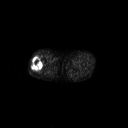
FDG PET of an extremity soft-tissue mass (from a PET/CT study), one axial slice. Slice 241 of 267 in the series (ordered by position). 3.27 mm slice thickness. 128 × 128 image matrix, field of view 700 × 700 mm. Male patient, age 43 years. From the clinical record (not read from this slice): histological type: poorly differentiated synovial sarcoma; grade: high; site of the primary tumour: right buttock.
Outlined on this slice (expert contour drawn on MRI and transferred to this co-registered scan by the dataset authors):
- gross tumour volume including surrounding oedema: bounding box <31,58,43,72> (left, top, right, bottom; pixels)
- gross tumour volume (mass): <31,58,43,72>